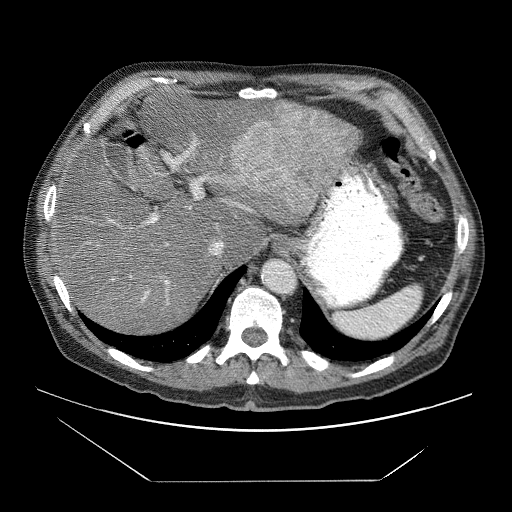
Contrast-enhanced abdominal CT (liver protocol), one axial slice. Slice 52 of 83 in the series (ordered by position). Reconstruction kernel STANDARD. Soft-tissue window (W 400 / L 40 HU). 2.5 mm slice thickness. 512 × 512 image matrix, field of view 420 × 420 mm. Case-level facts recorded for this patient, not image findings: diagnosis: hepatocellular carcinoma (patient treated with transarterial chemoembolisation; whether this scan precedes or follows treatment is not stated here); TNM stage (as recorded): Stage-IVB; Child-Pugh class: B; tumour differentiation: poorly differentiated; tumour nodularity: uninodular.
Outlined on this slice (semi-automatic segmentation, software-assisted and operator-edited):
- liver parenchyma outside the tumour (the mass and vessels are separate outlines, so this box may not span the whole liver): bounding box <52,84,361,332> (left, top, right, bottom; pixels)
- mass: <233,102,356,220>
- liver vessels: <86,139,252,304>